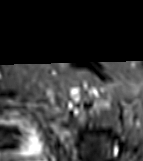
MRI of an extremity soft-tissue mass, one axial slice; slice 64 of 81 in the series (ordered by position); STIR; MR volume resampled by the dataset authors to the PET/CT grid (not the native acquisition matrix); 3.27 mm slice thickness; 143 × 161 image matrix, field of view 140 × 157 mm. Female patient. Case-level facts recorded for this patient, not image findings: histological type: myxofibrosarcoma; grade: intermediate; site of the primary tumour: left thigh.
Structures marked on this image (expert contour drawn on MRI and transferred to this co-registered scan by the dataset authors):
- gross tumour volume including surrounding oedema: bounding box [x1, y1, x2, y2] px = [70, 95, 80, 105]